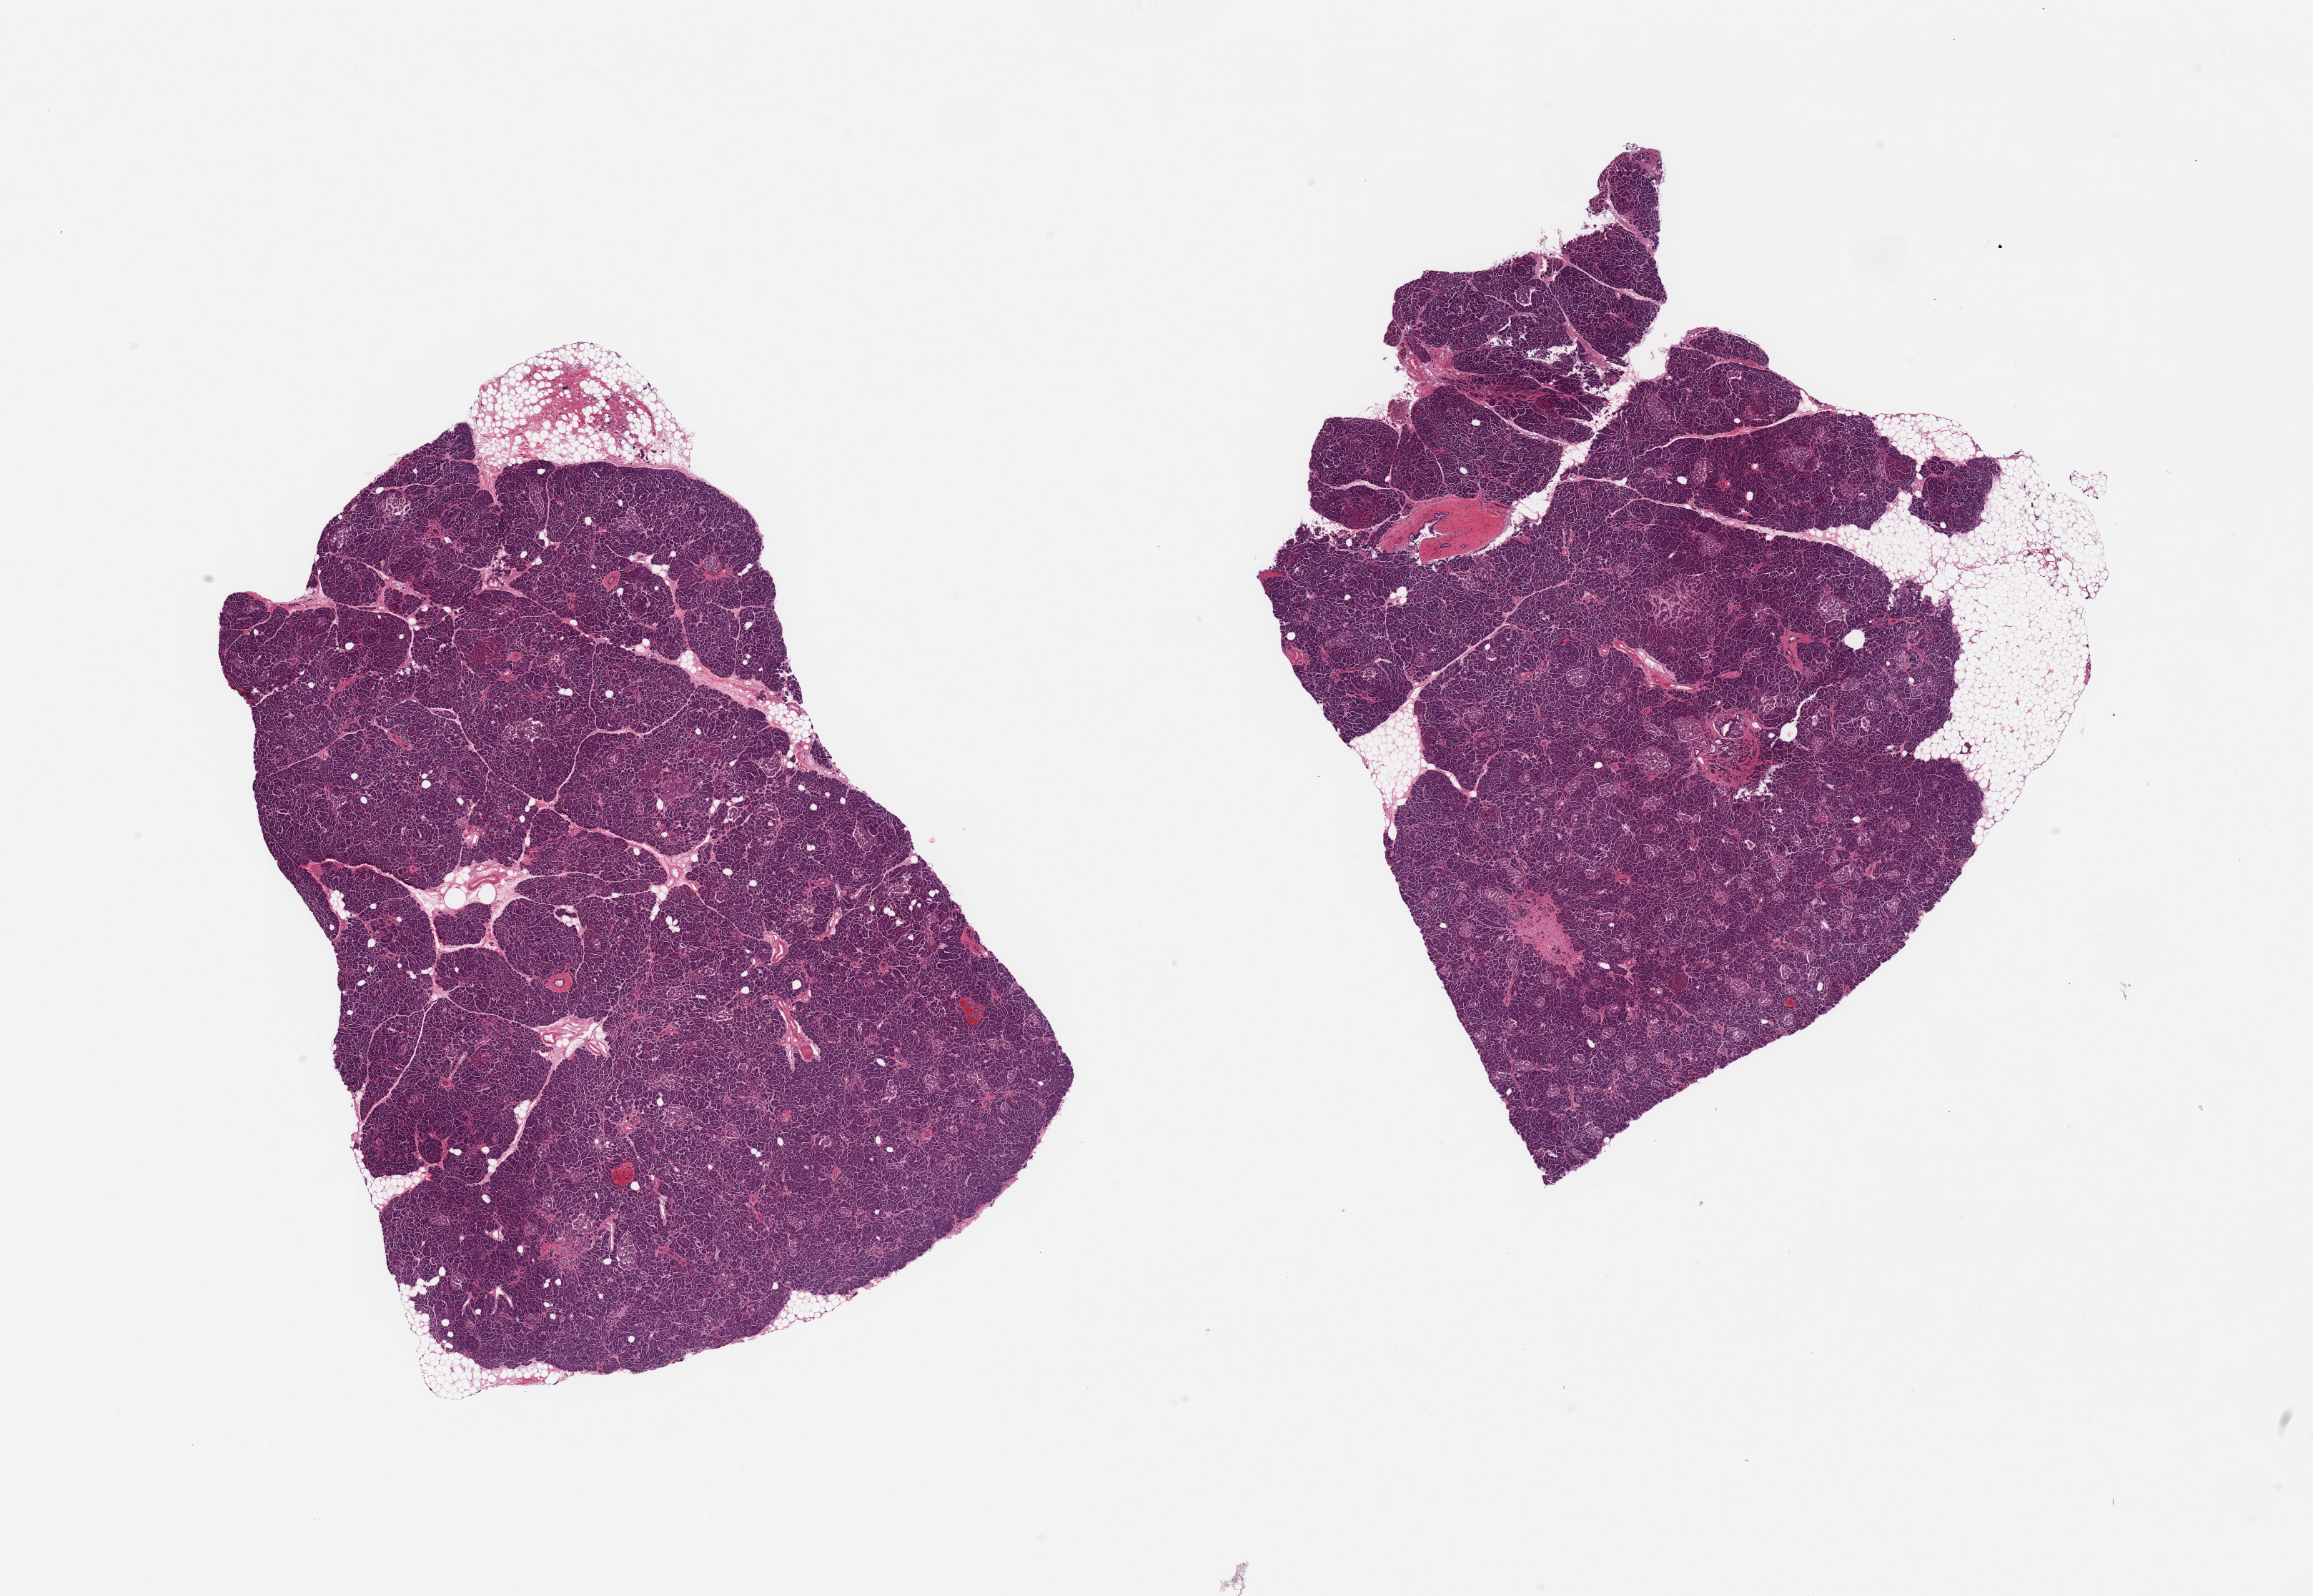
Whole-slide image, H&E stain, whole scanned area (about 25.6 x 17.7 mm, acquisition: 20x scan) shown as a low-resolution overview, PAXgene-fixed, paraffin-embedded tissue, sampled site (target tissue): pancreas, tissue donor sample. Donor sex: male.
Review note (as recorded): 2 pieces; increased number of islets; foci of fibrosis and ductal proliferation c/w chronic 2inflammation; sample may be near tail of pancreas.